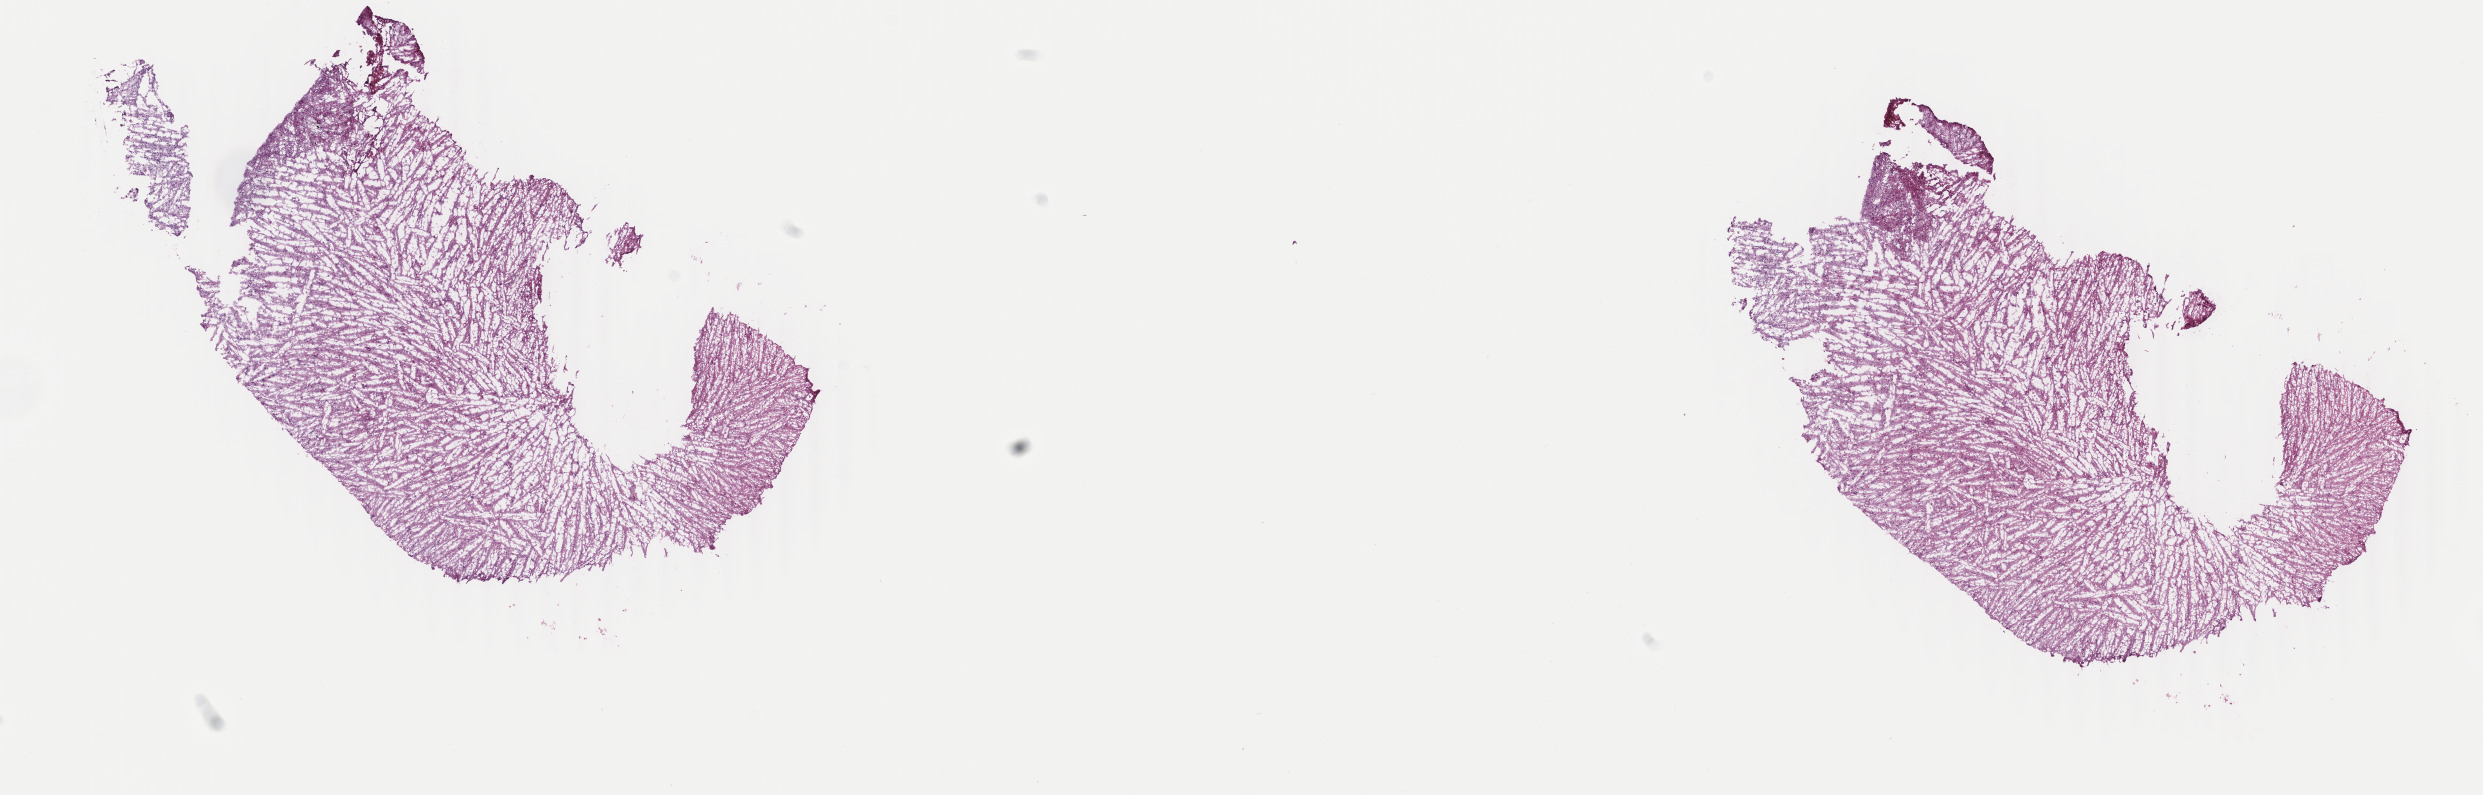
Digitized H&E tissue section (whole slide) — a low-resolution overview of the entire scanned area, about 19.8 x 6.3 mm; frozen section from the top of the tissue portion; primary tumour sample from the brain. Male, age 69 years at initial diagnosis. Histologic grade: G3 (poorly differentiated). Composition of this section per pathologist review: tumour cells 40%, tumour nuclei 90%, normal cells 10%, stromal cells 50%, necrosis 0%. Infiltration values recorded for this section: lymphocyte infiltration 0%, monocyte infiltration 0%, neutrophil infiltration 0%.
Histologic diagnosis: Astrocytoma, anaplastic (cerebrum).